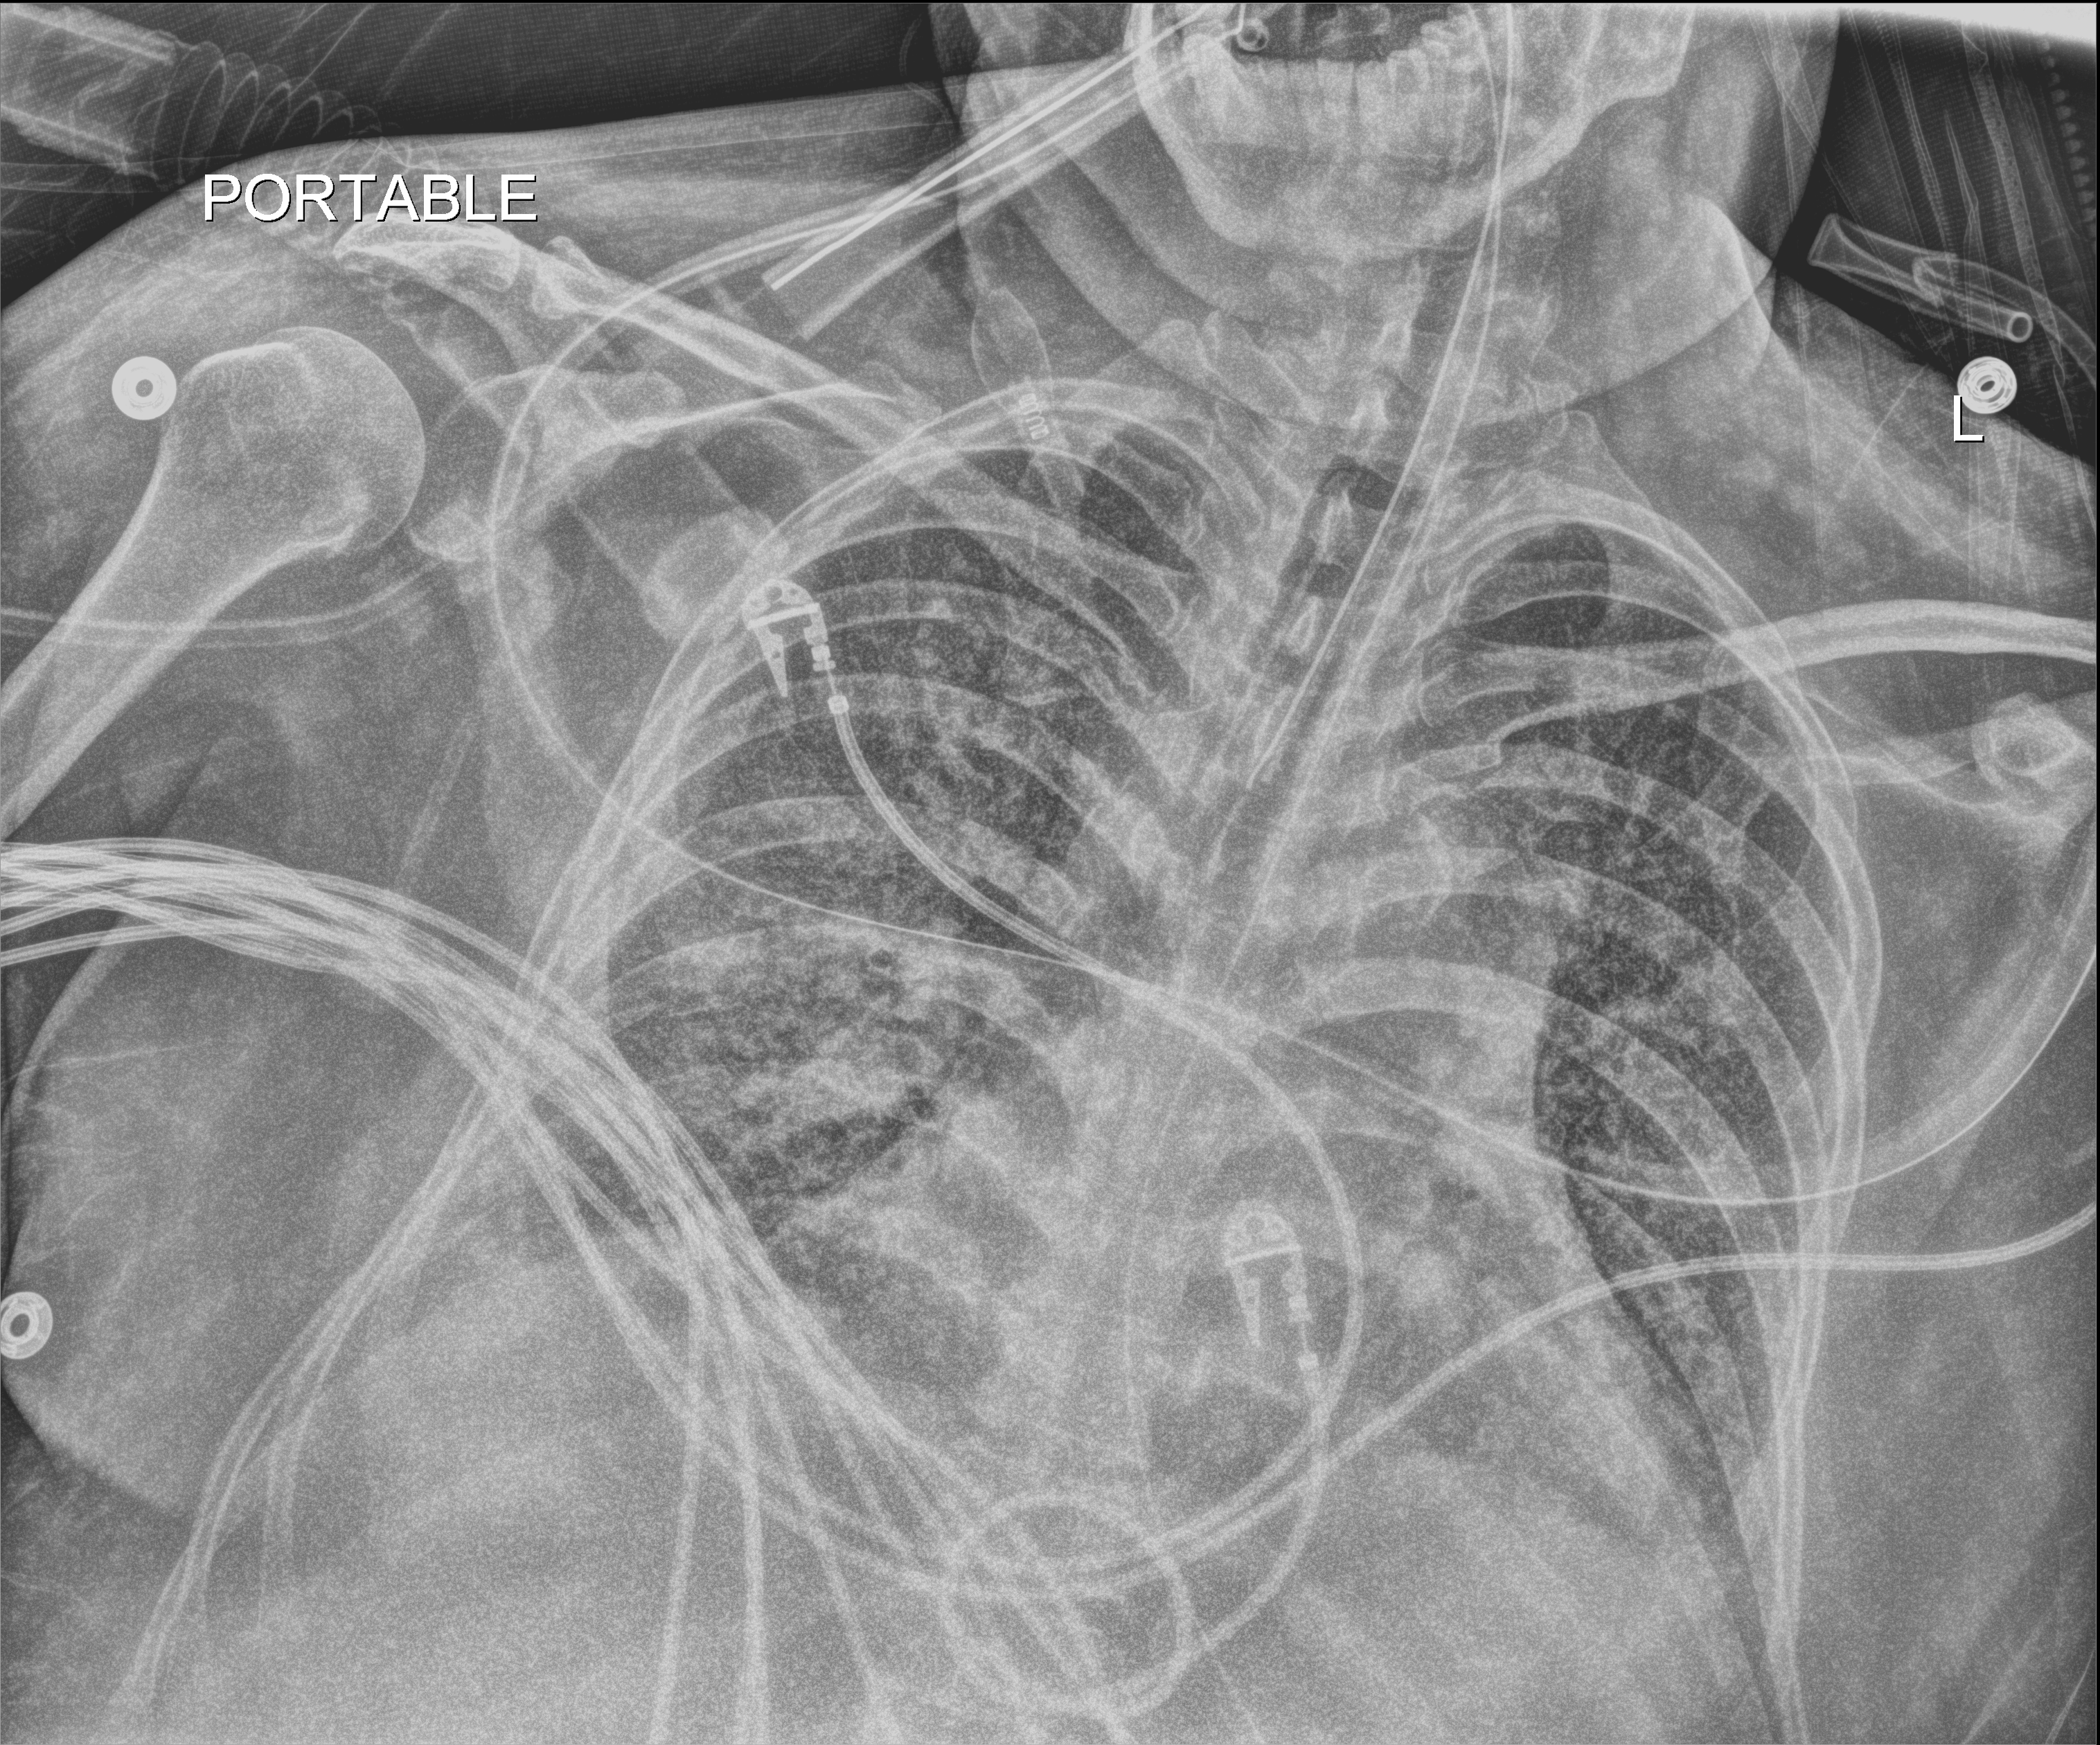
Bedside chest radiograph (digital radiography); anteroposterior (AP) projection. Adult patient hospitalised with COVID-19, age 18–59 years.
From the hospital-stay record, not from the radiograph (when in the stay this image was taken is not recorded): hypertension (admission record): no; other chronic lung disease (admission record): no.